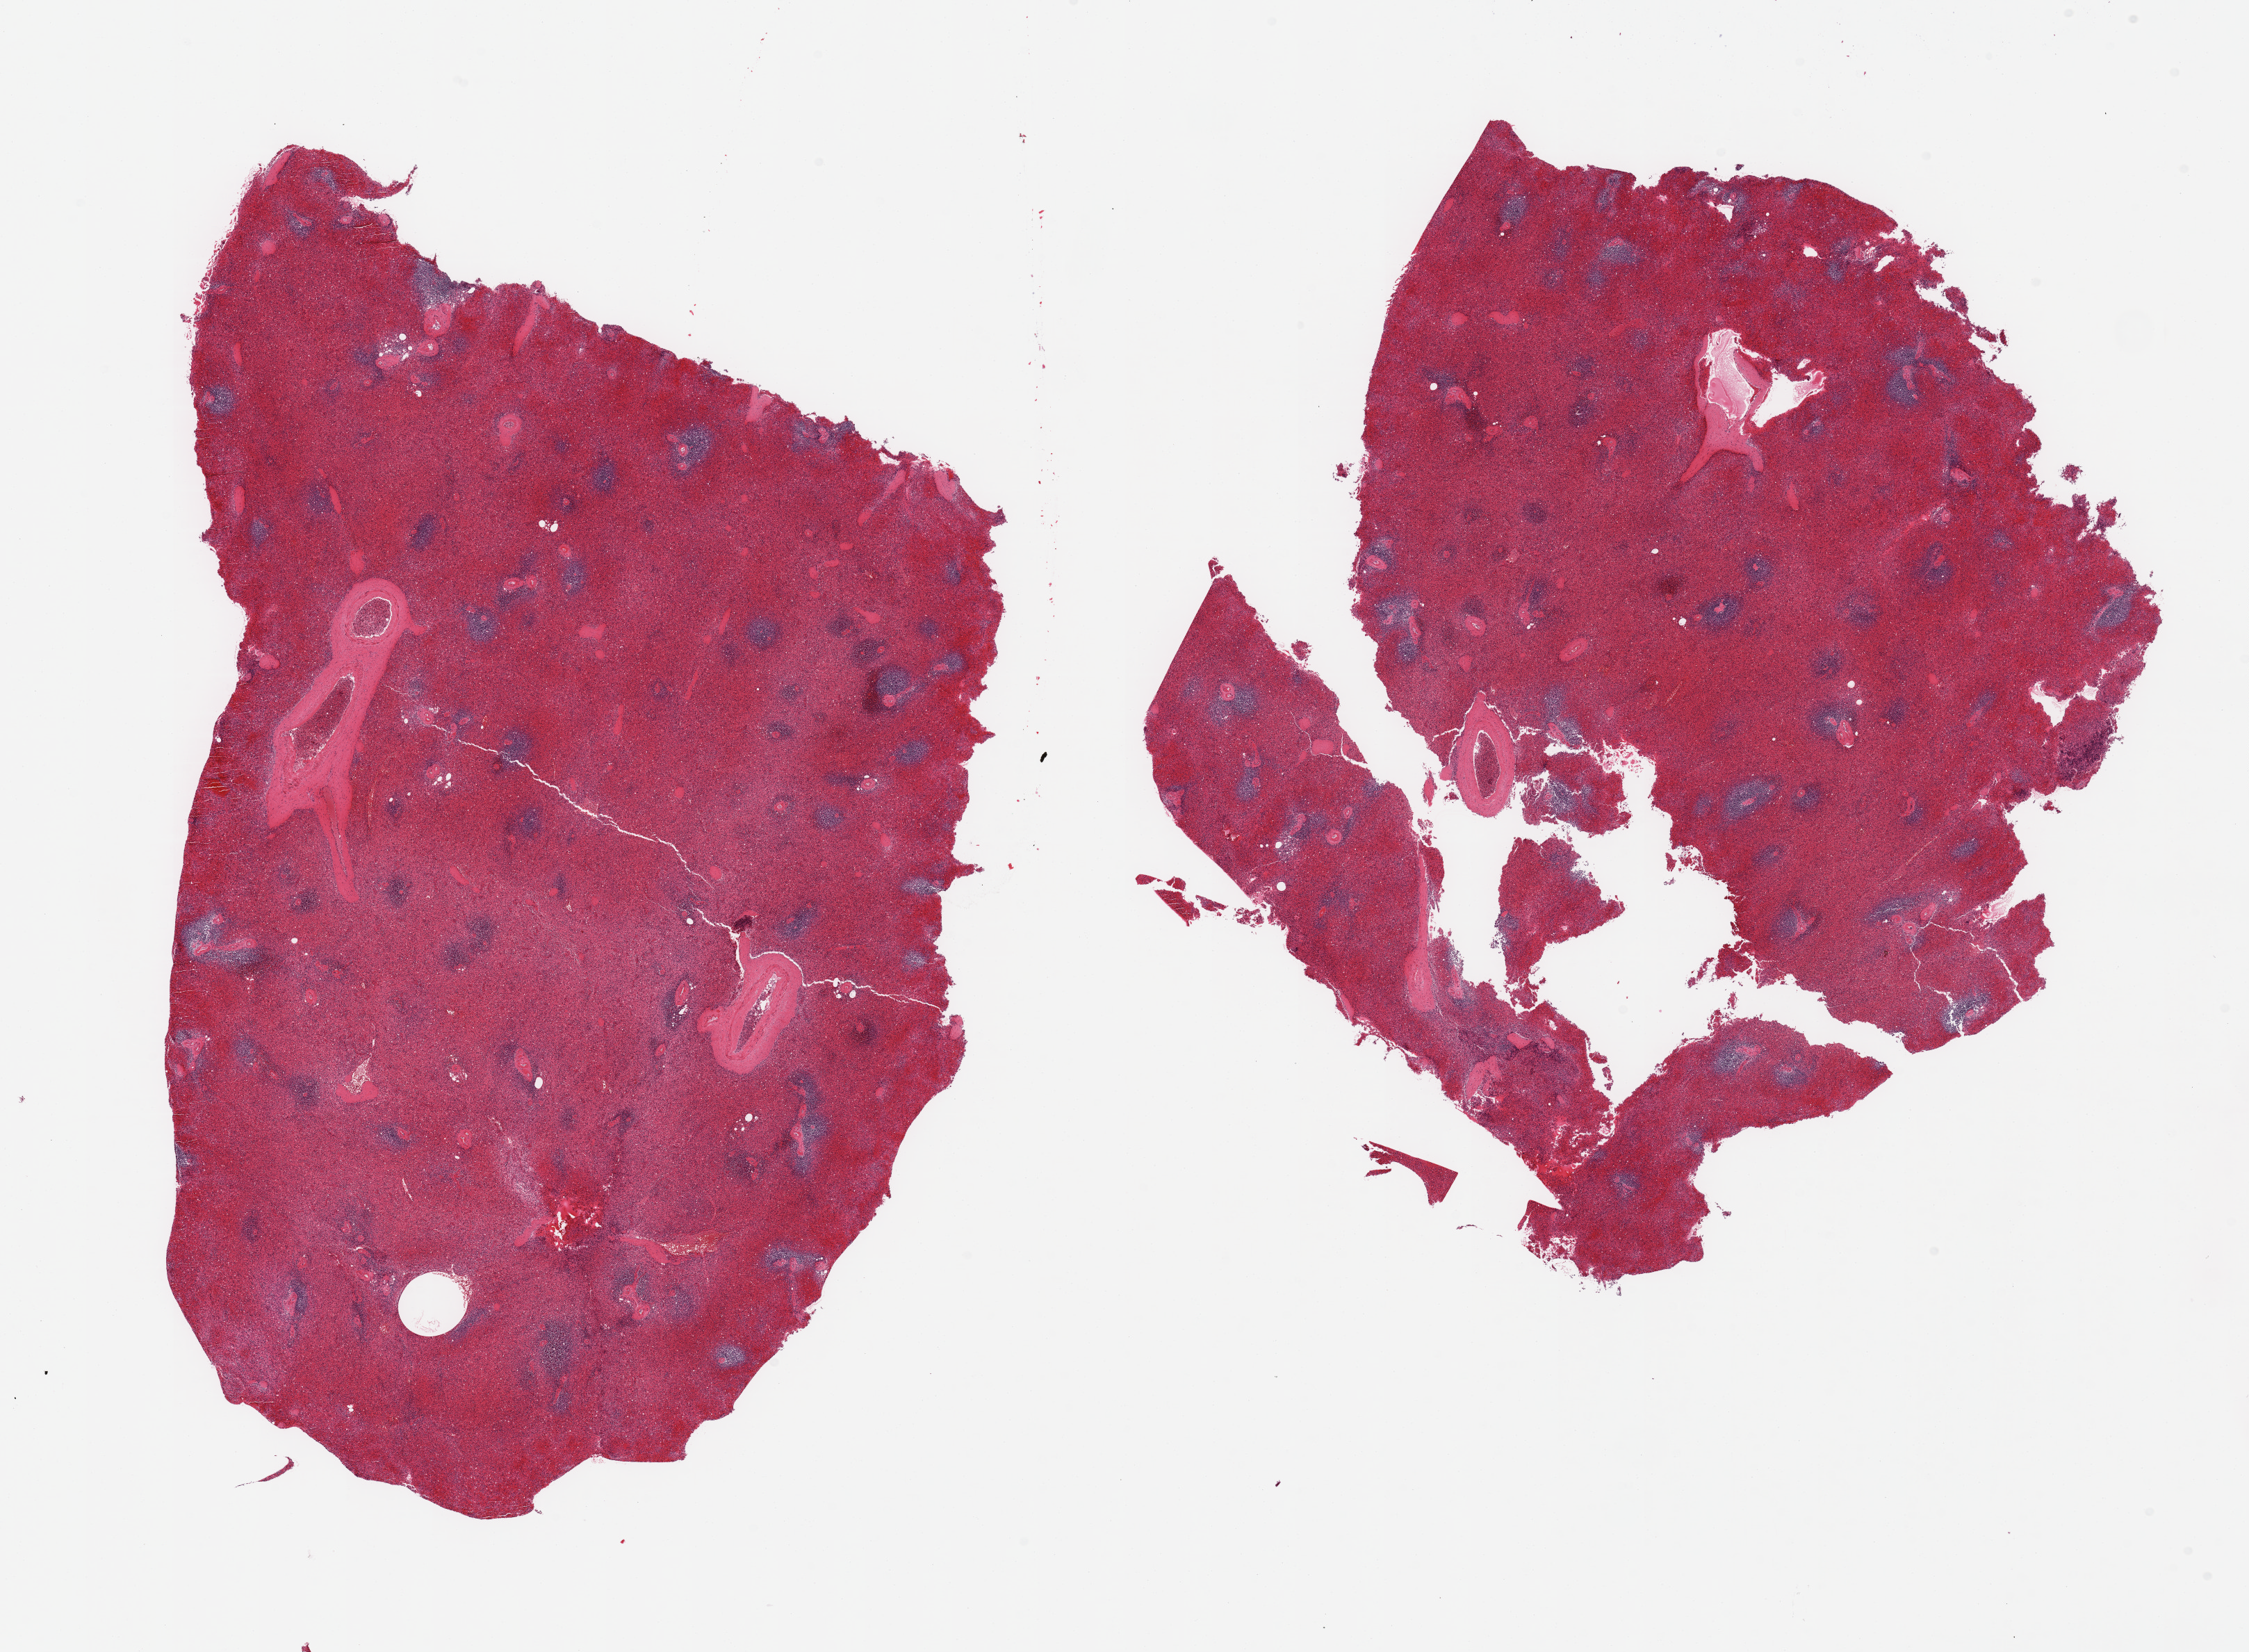
Whole-slide image, hematoxylin and eosin (H&E) stain — whole scanned area (about 25.6 x 18.8 mm, slide scanned at 20x) shown as a low-resolution overview, PAXgene-fixed, paraffin-embedded tissue, section of spleen (target tissue), tissue donor sample.
* reviewer comment on this tissue sample: 2 pieces, marked congestion